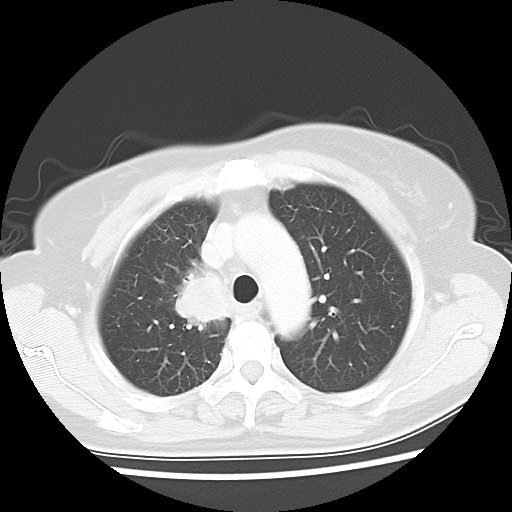
Chest CT, one axial slice; slice 43 of 56 in the series (ordered by position); lung window (W 1500 / L -600 HU); 5 mm slice thickness; 512 × 512 image matrix, field of view 314 × 314 mm. Female patient, age 62 years. From the clinical record (not read from this slice): clinical TNM (as recorded): T2 N1 M1a.
Structures marked on this image (bounding box drawn by a radiologist):
- lung tumour (recorded histology: adenocarcinoma): bounding box (x1, y1, x2, y2) in pixels: (158, 256, 234, 335)